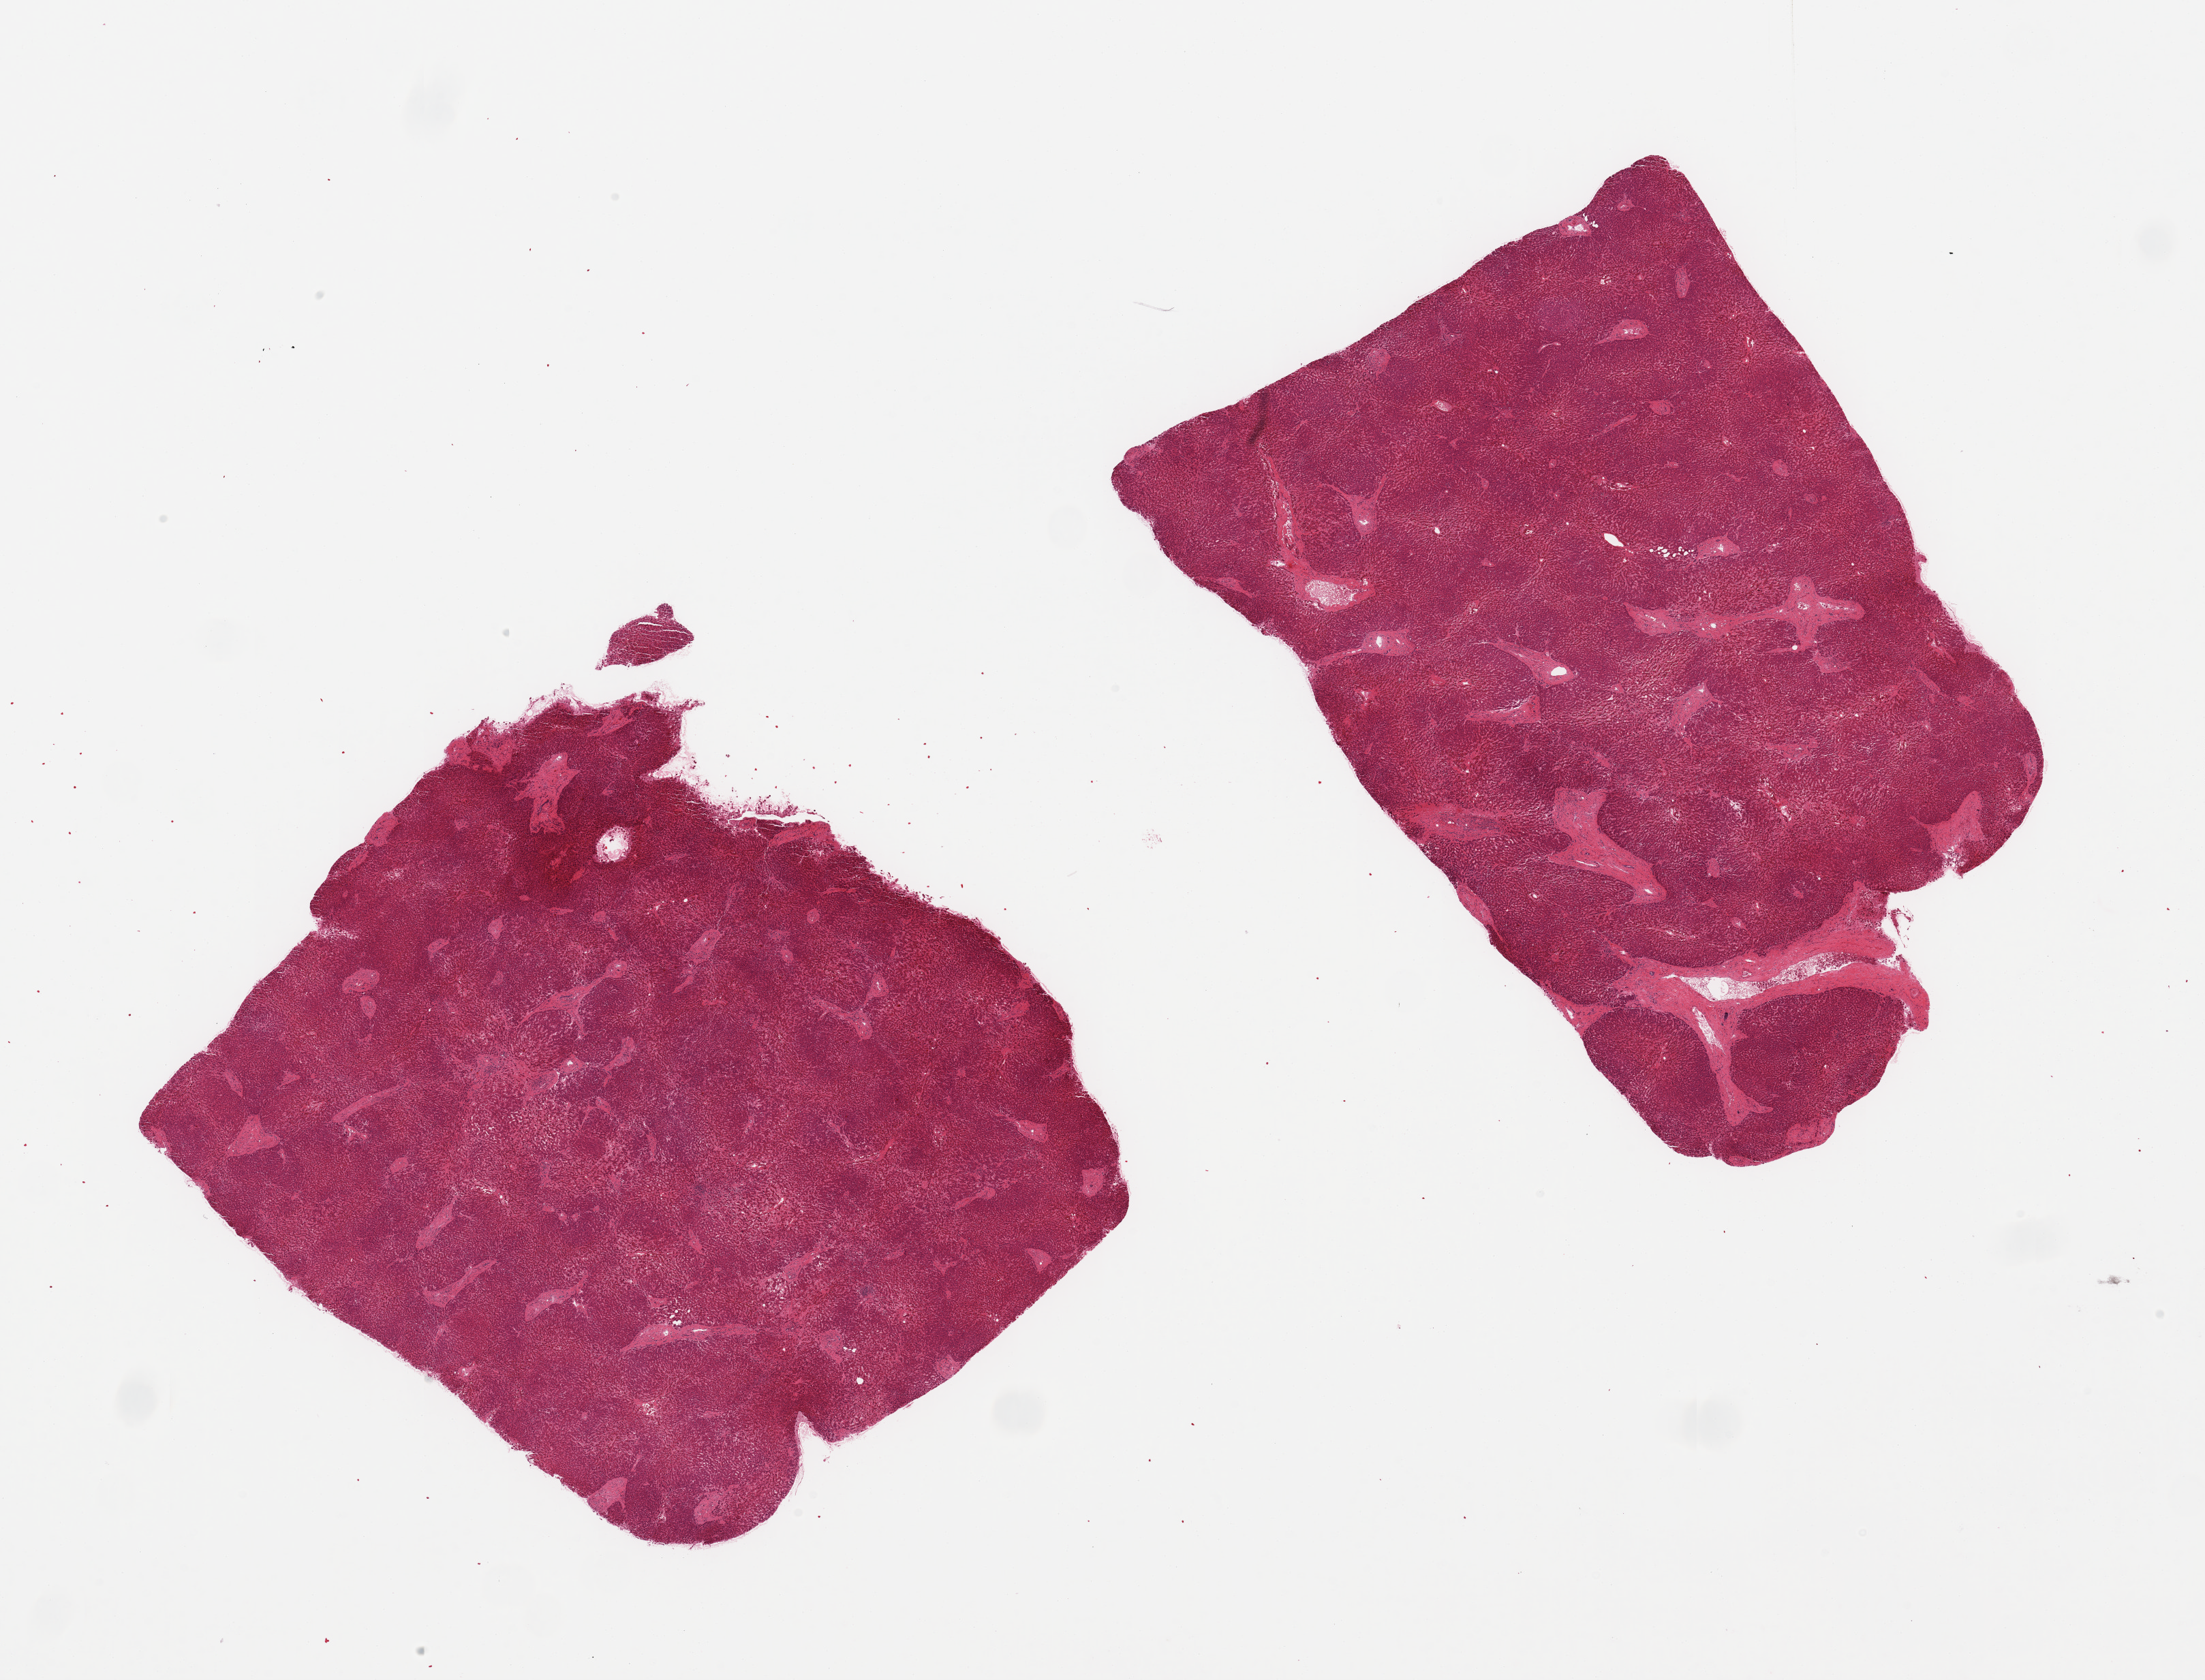
Hematoxylin and eosin (H&E) whole-slide image — a low-resolution overview of the entire scanned area, about 25.6 x 19.5 mm (slide scanned at 20x). PAXgene-fixed paraffin-embedded (PFPE) section. Sampled site (target tissue): liver. Donor tissue sample. Donor sex: male.
Reviewer comment on this tissue sample: 2 pieces; central congestion, some fibrosis.